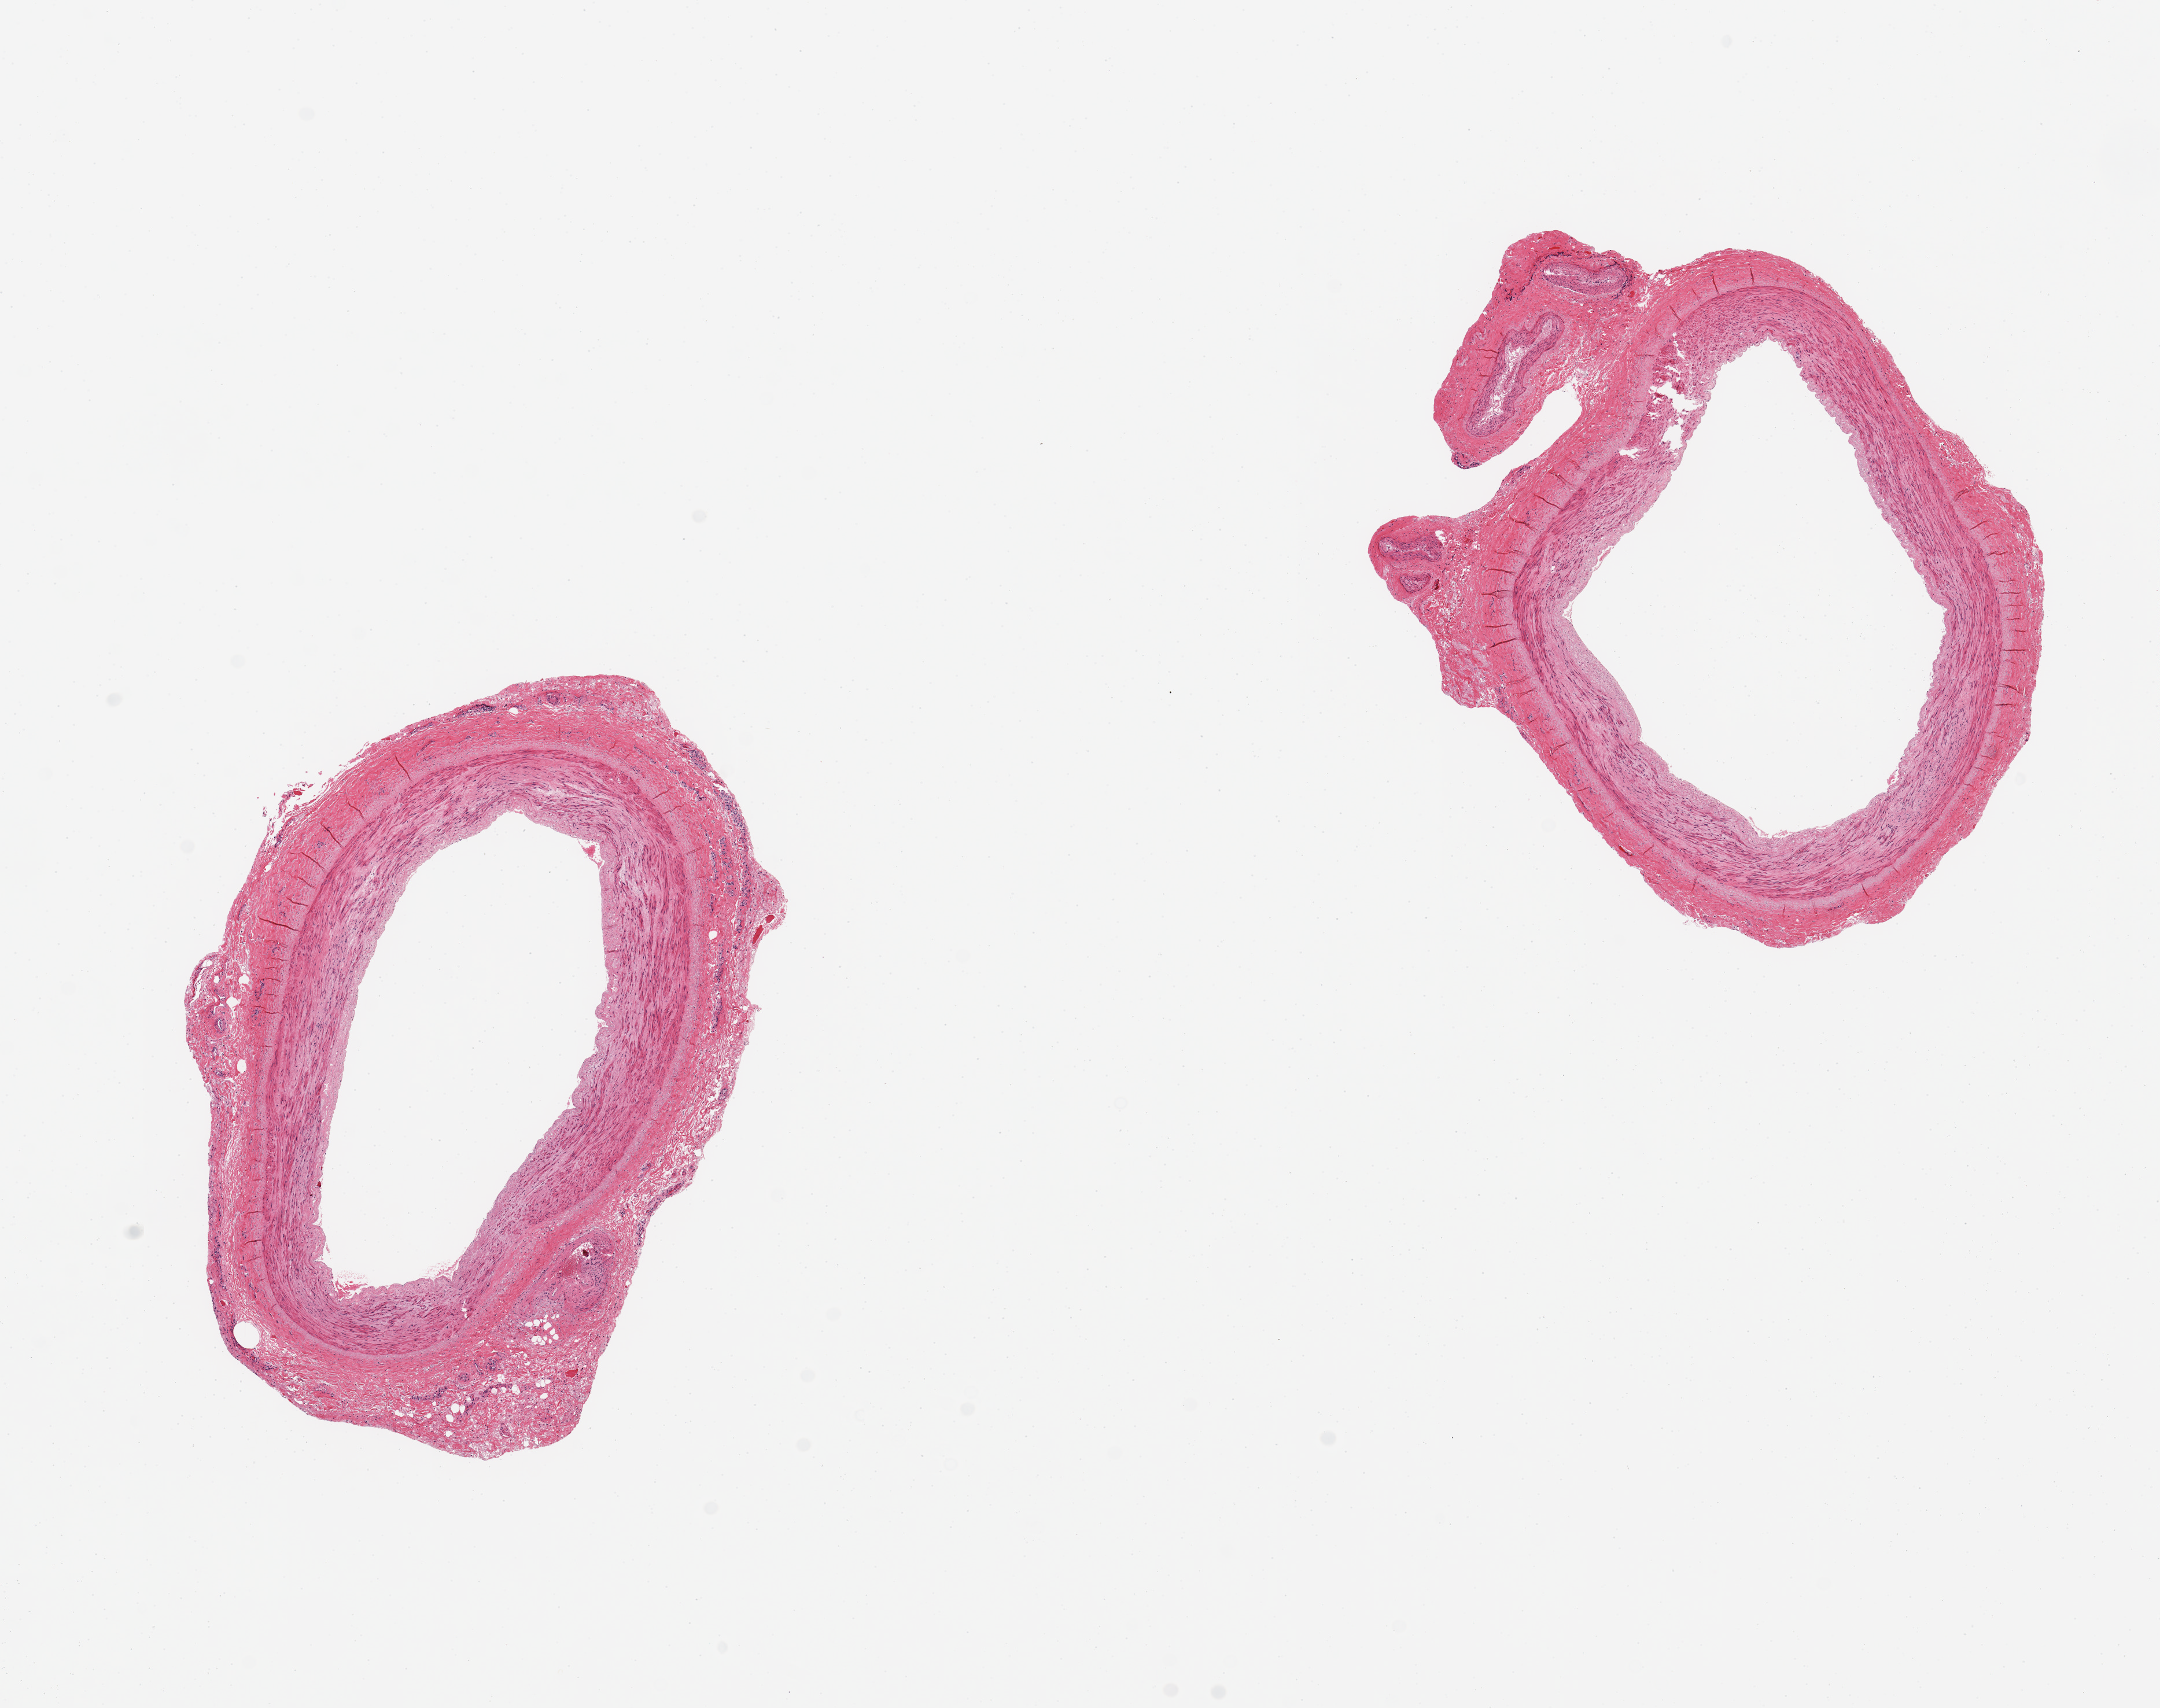
Digitized haematoxylin and eosin-stained section, whole scanned area (about 14.8 x 11.7 mm, acquisition: 20x scan) shown as a low-resolution overview; PAXgene-fixed, paraffin-embedded tissue; target tissue: tibial artery; tissue donor sample. Donor sex: female.
Review note (as recorded): 2 ~5mm d aliquots???good clean specimens.